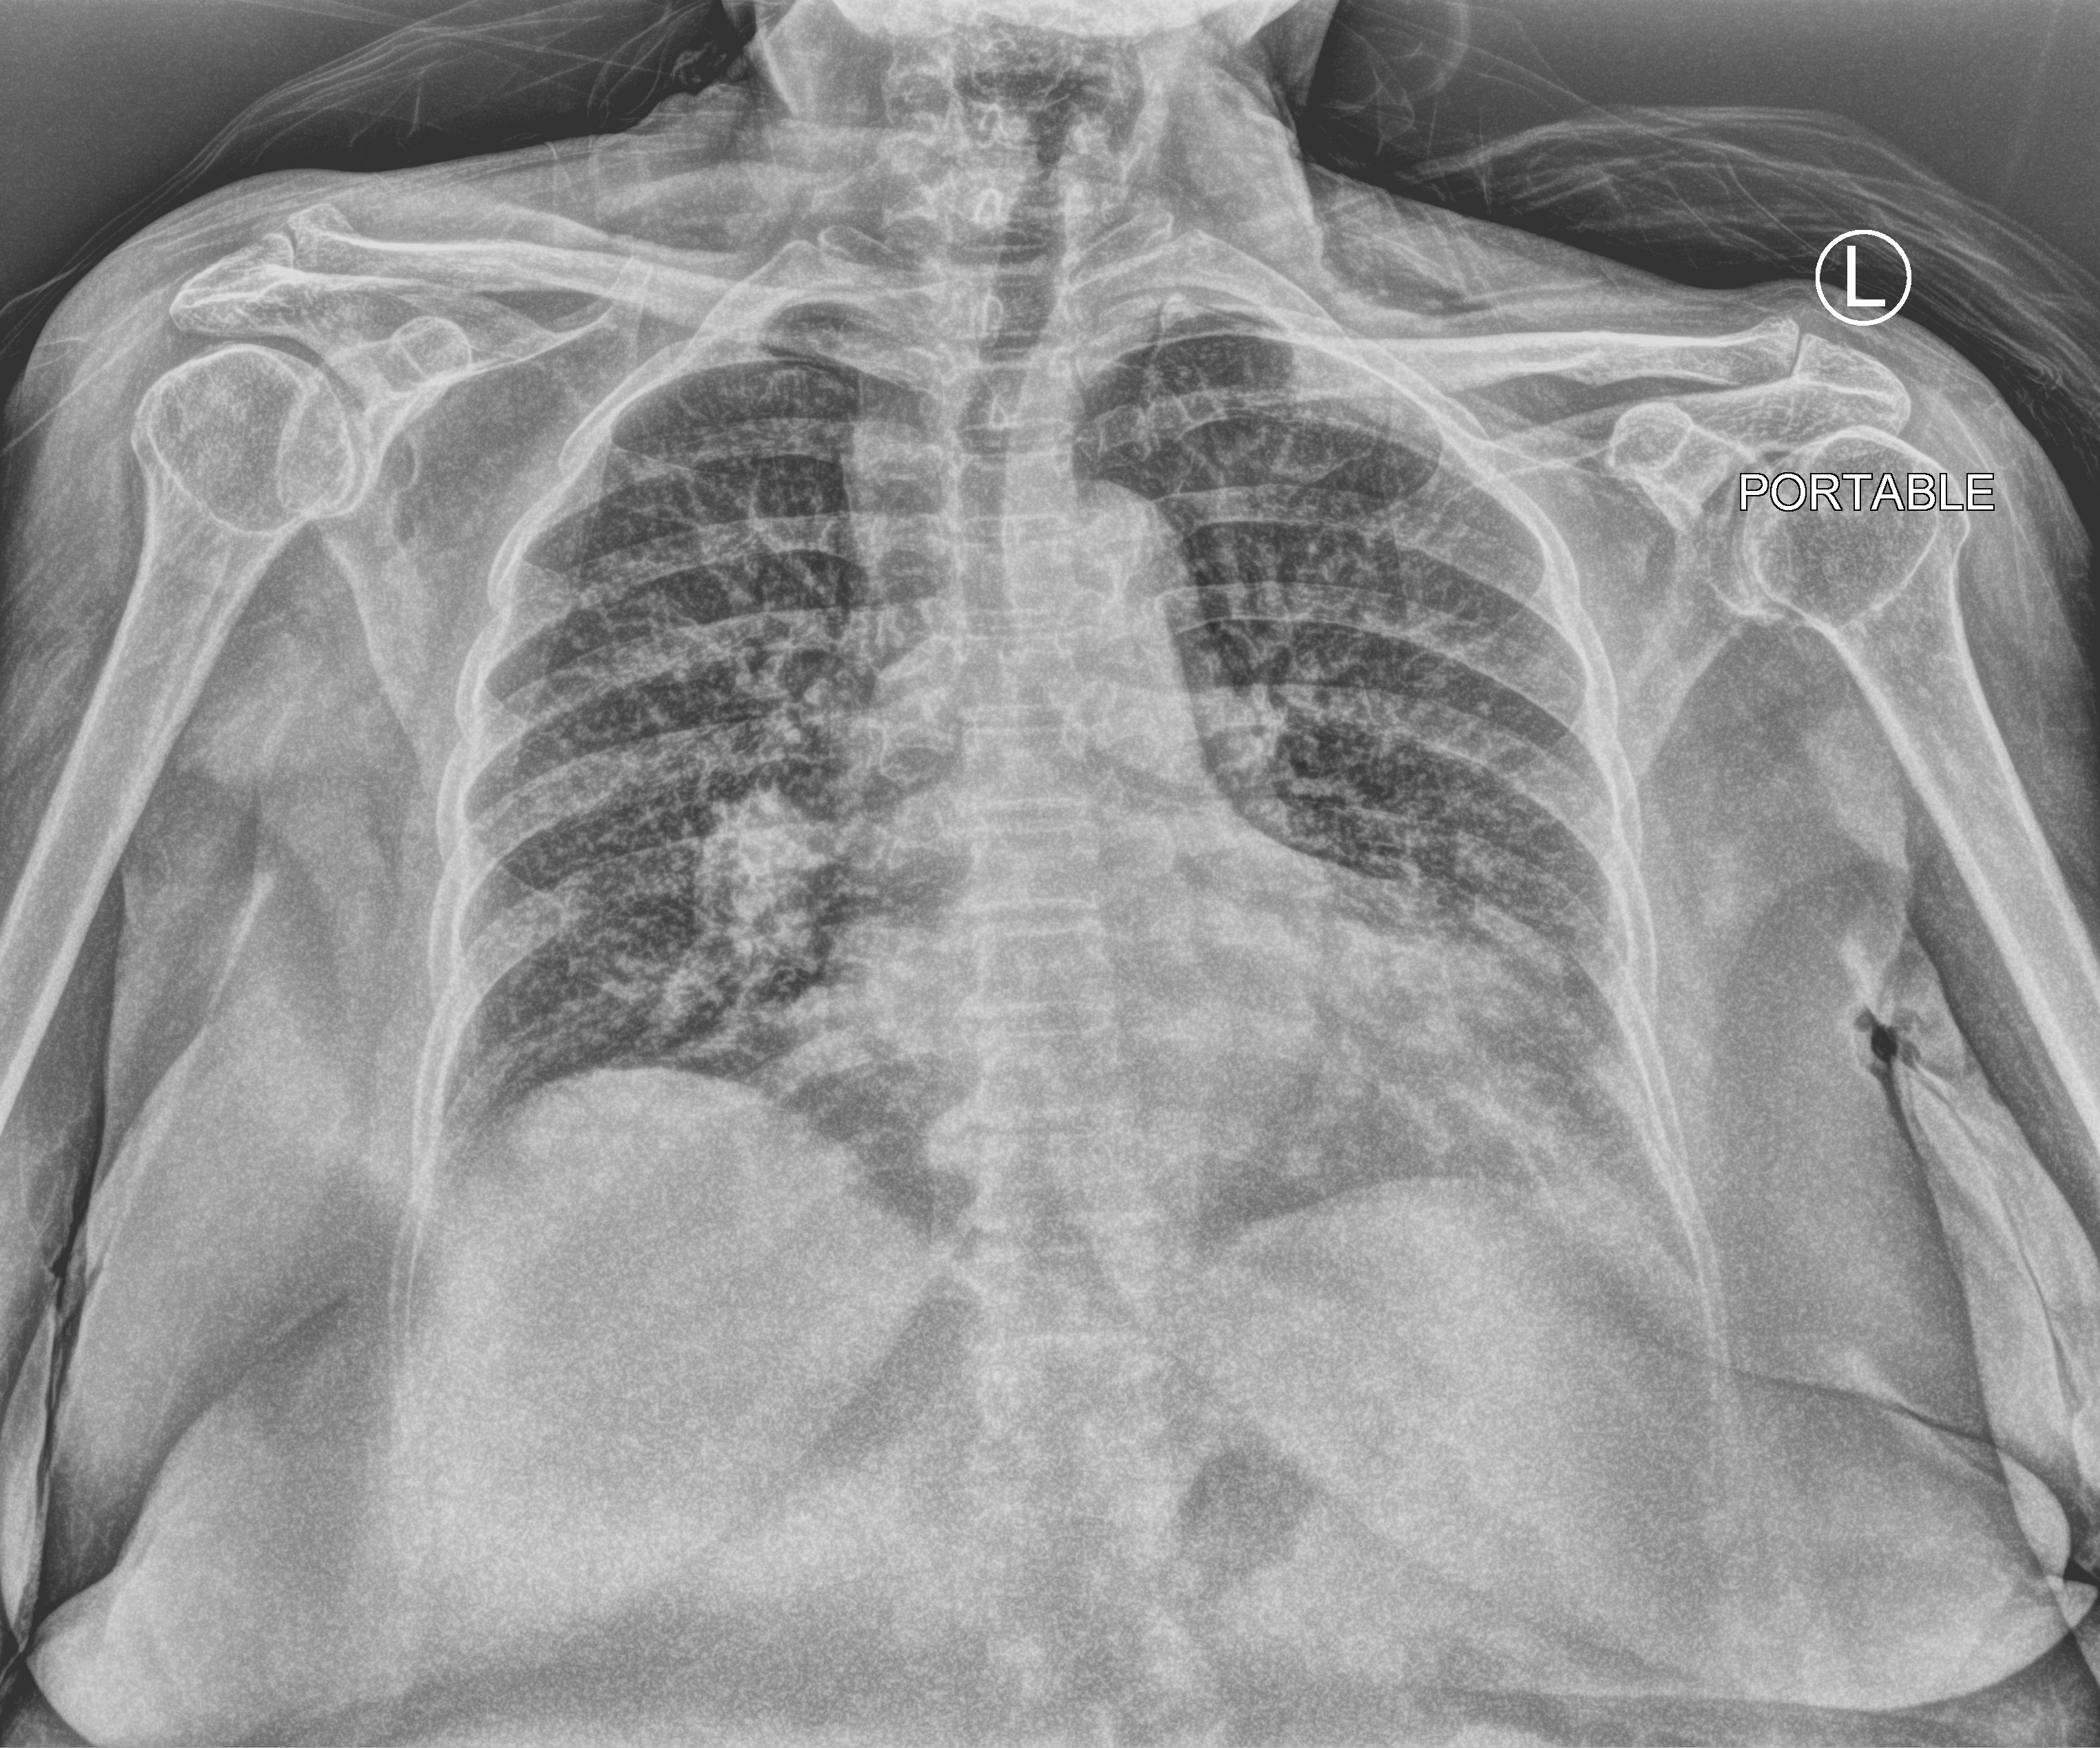
Chest X-ray (portable), anteroposterior (AP) projection. Female patient hospitalised with COVID-19, age 75–90 years.
Hospital-stay facts (about this admission, not read from this image; timing relative to this image not recorded):
- mechanically ventilated during this hospital stay: no
- admitted to intensive care during this hospital stay: no